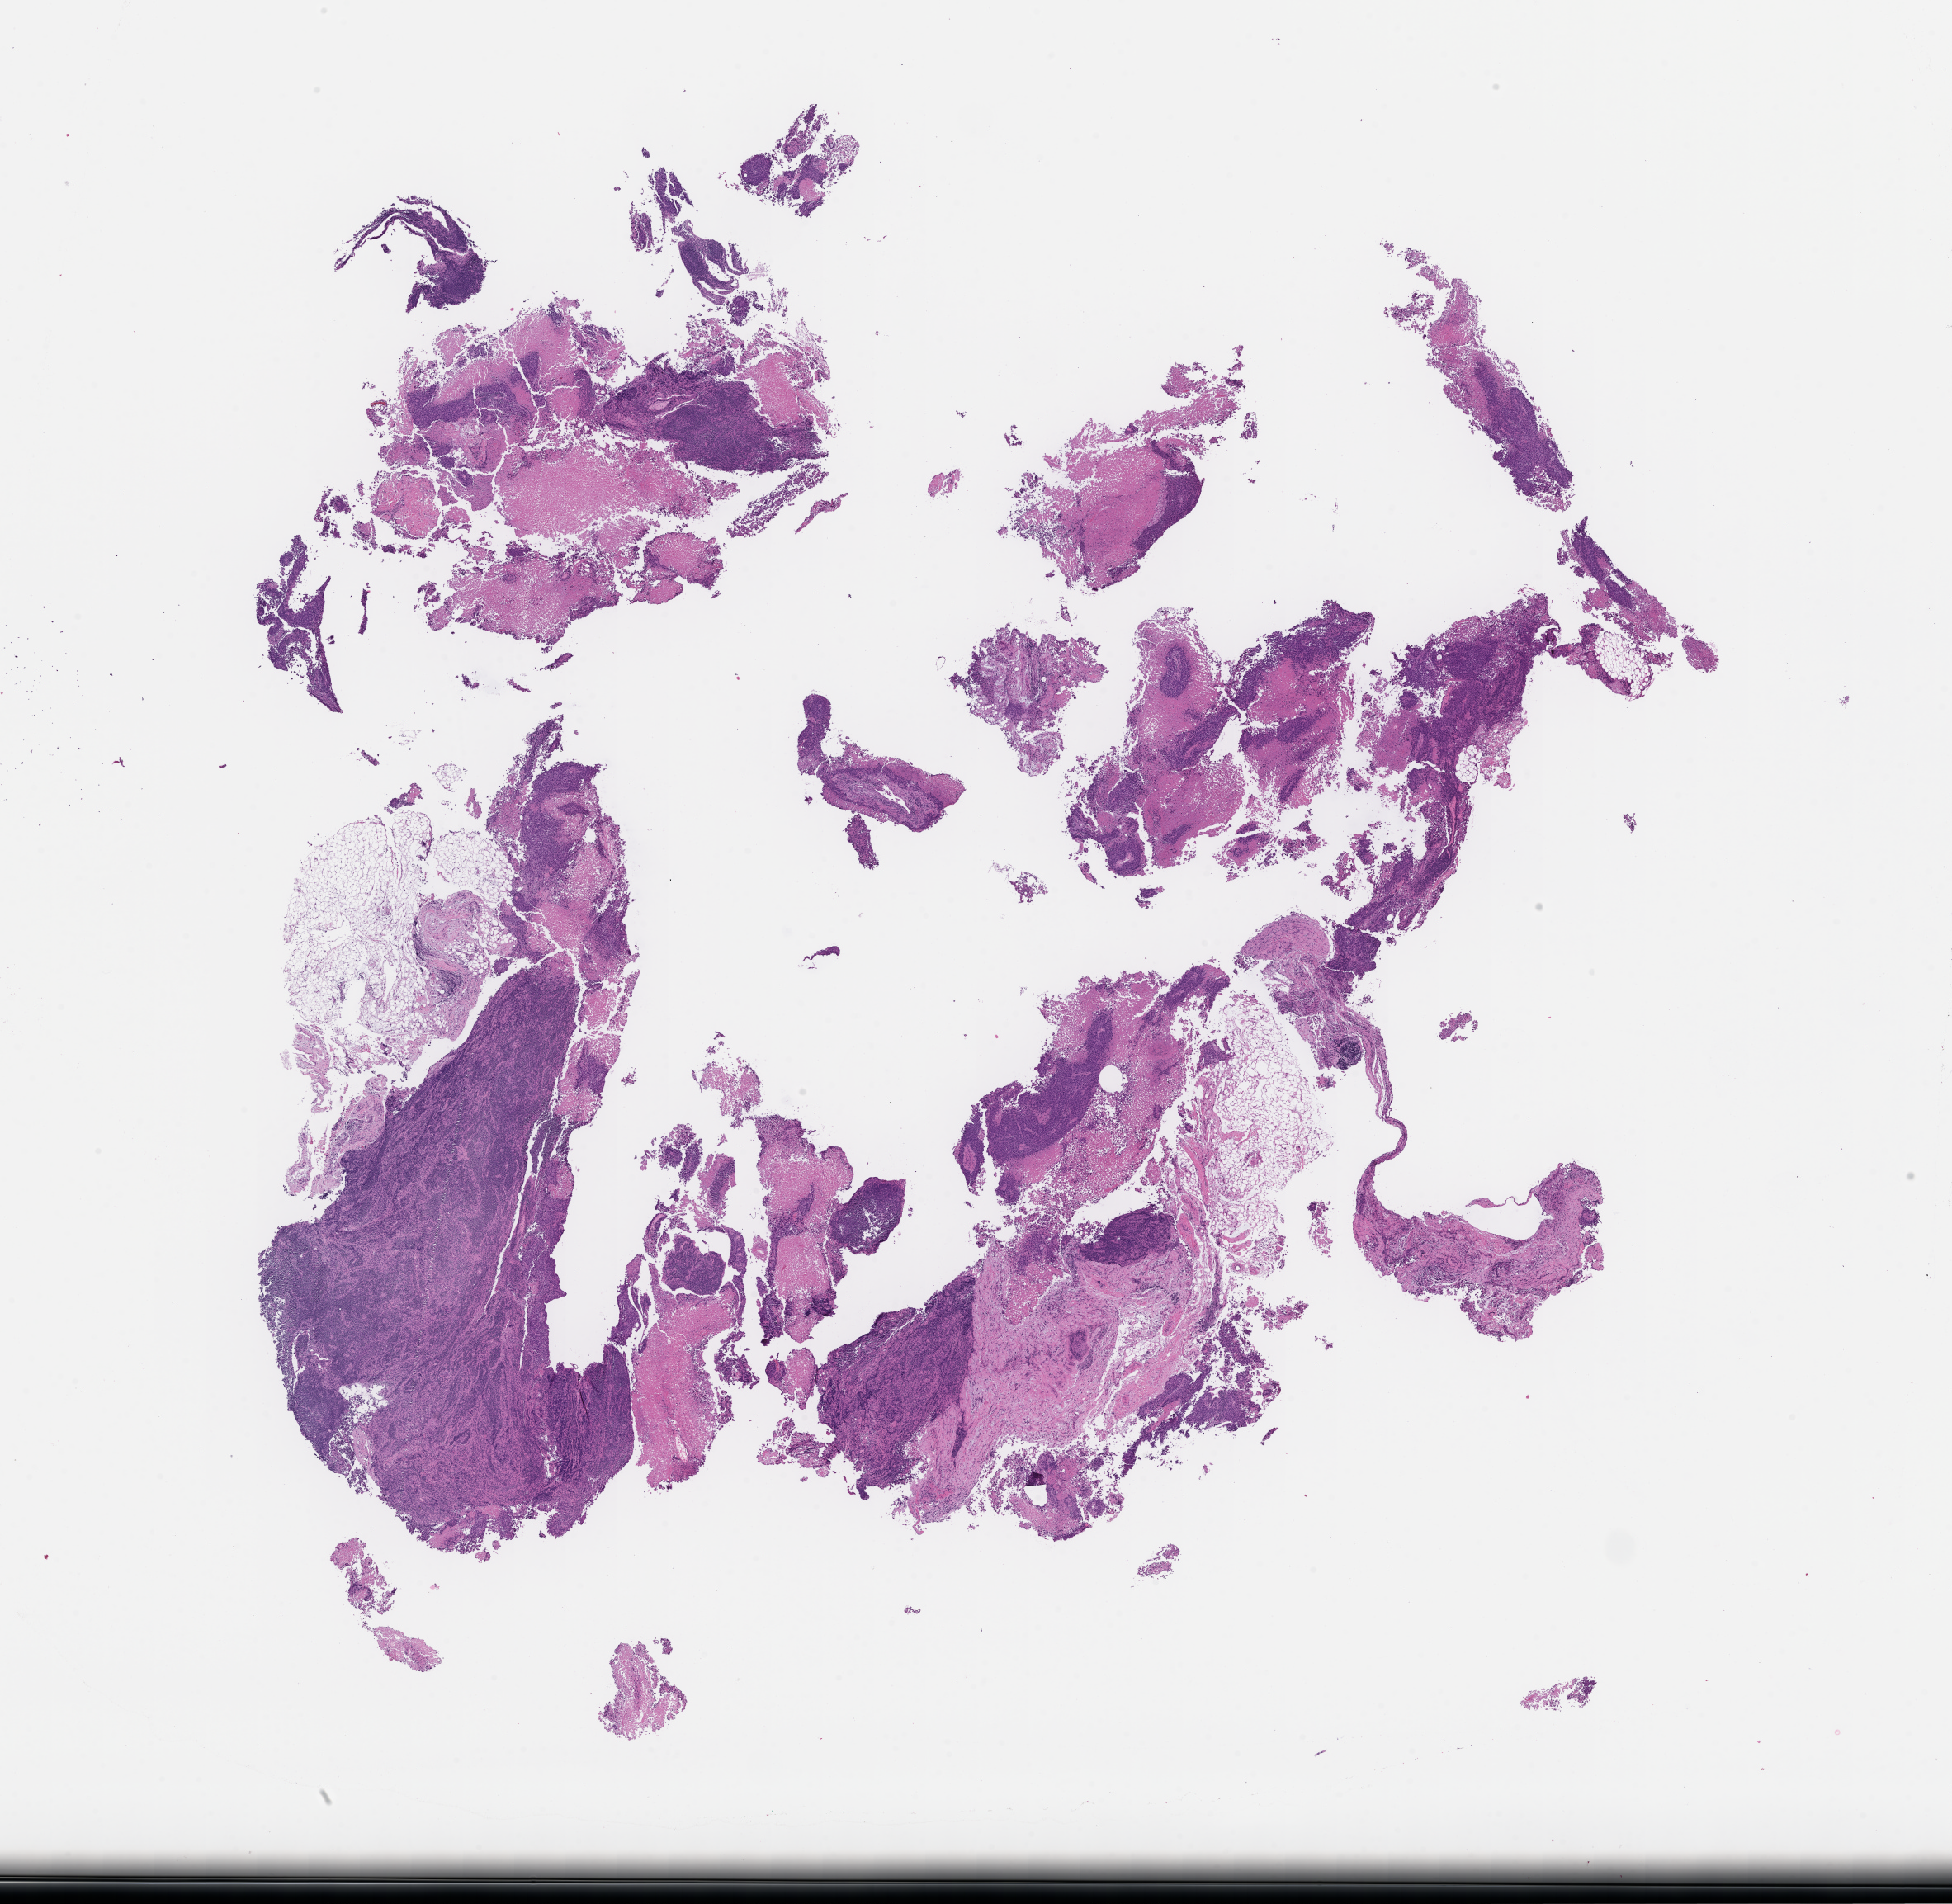
Whole-slide image, H&E stain, low-resolution overview of the scanned area, about 19.1 x 18.6 mm, formalin-fixed, paraffin-embedded (FFPE) tissue, tissue site: lung, specimen time point: archival tissue. Male patient.
This section: primary tumor. Diagnosis: Non-Small Cell Lung Carcinoma.